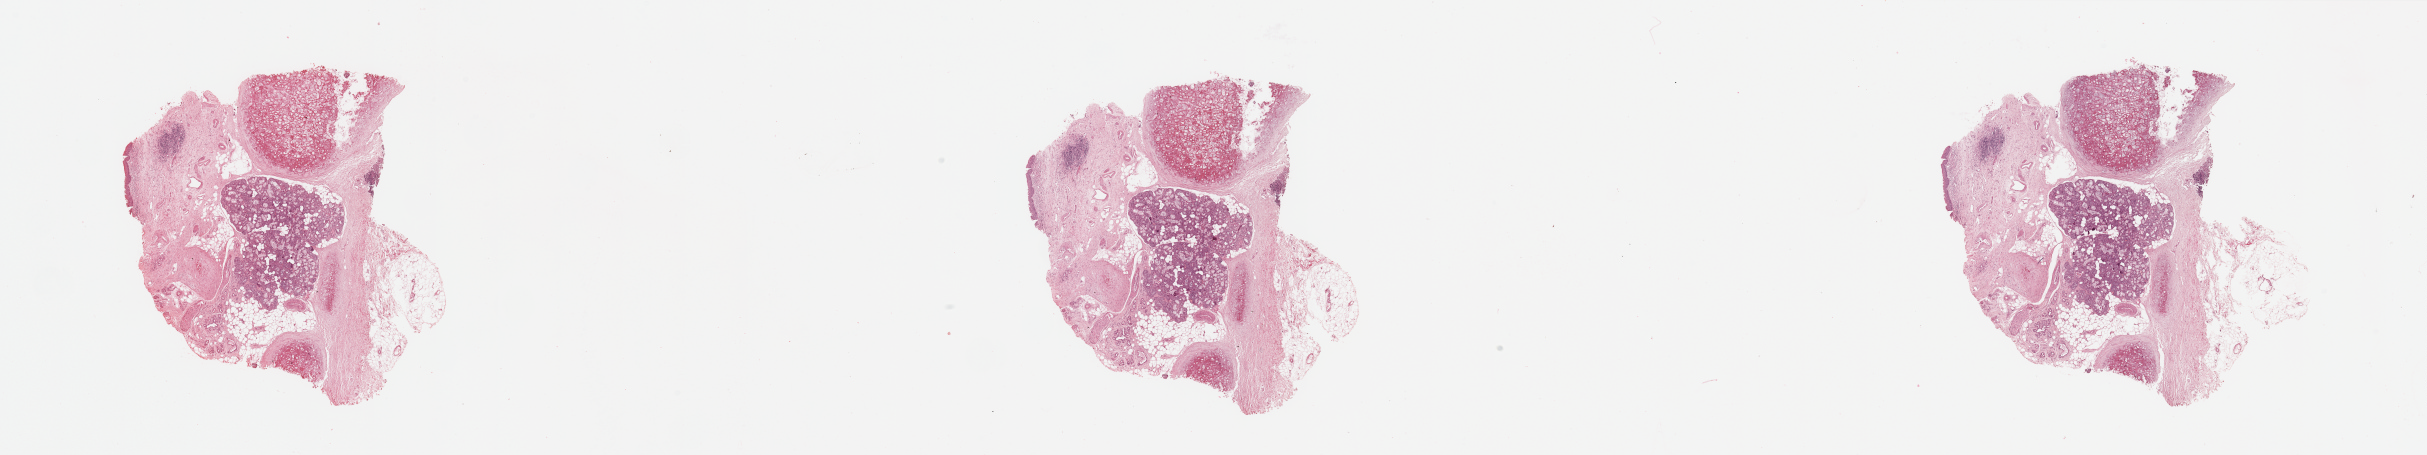
Digitized Hematoxylin and eosin (H&E) stained tissue section (whole slide) — a low-resolution overview of the entire scanned area, about 38.4 x 7.2 mm. Normal (non-tumour) tissue sample, sampled site: larynx. 60-year-old male patient.
This section: normal (non-tumour) tissue from the same patient. Patient diagnosis: Squamous cell carcinoma, NOS (larynx, NOS).